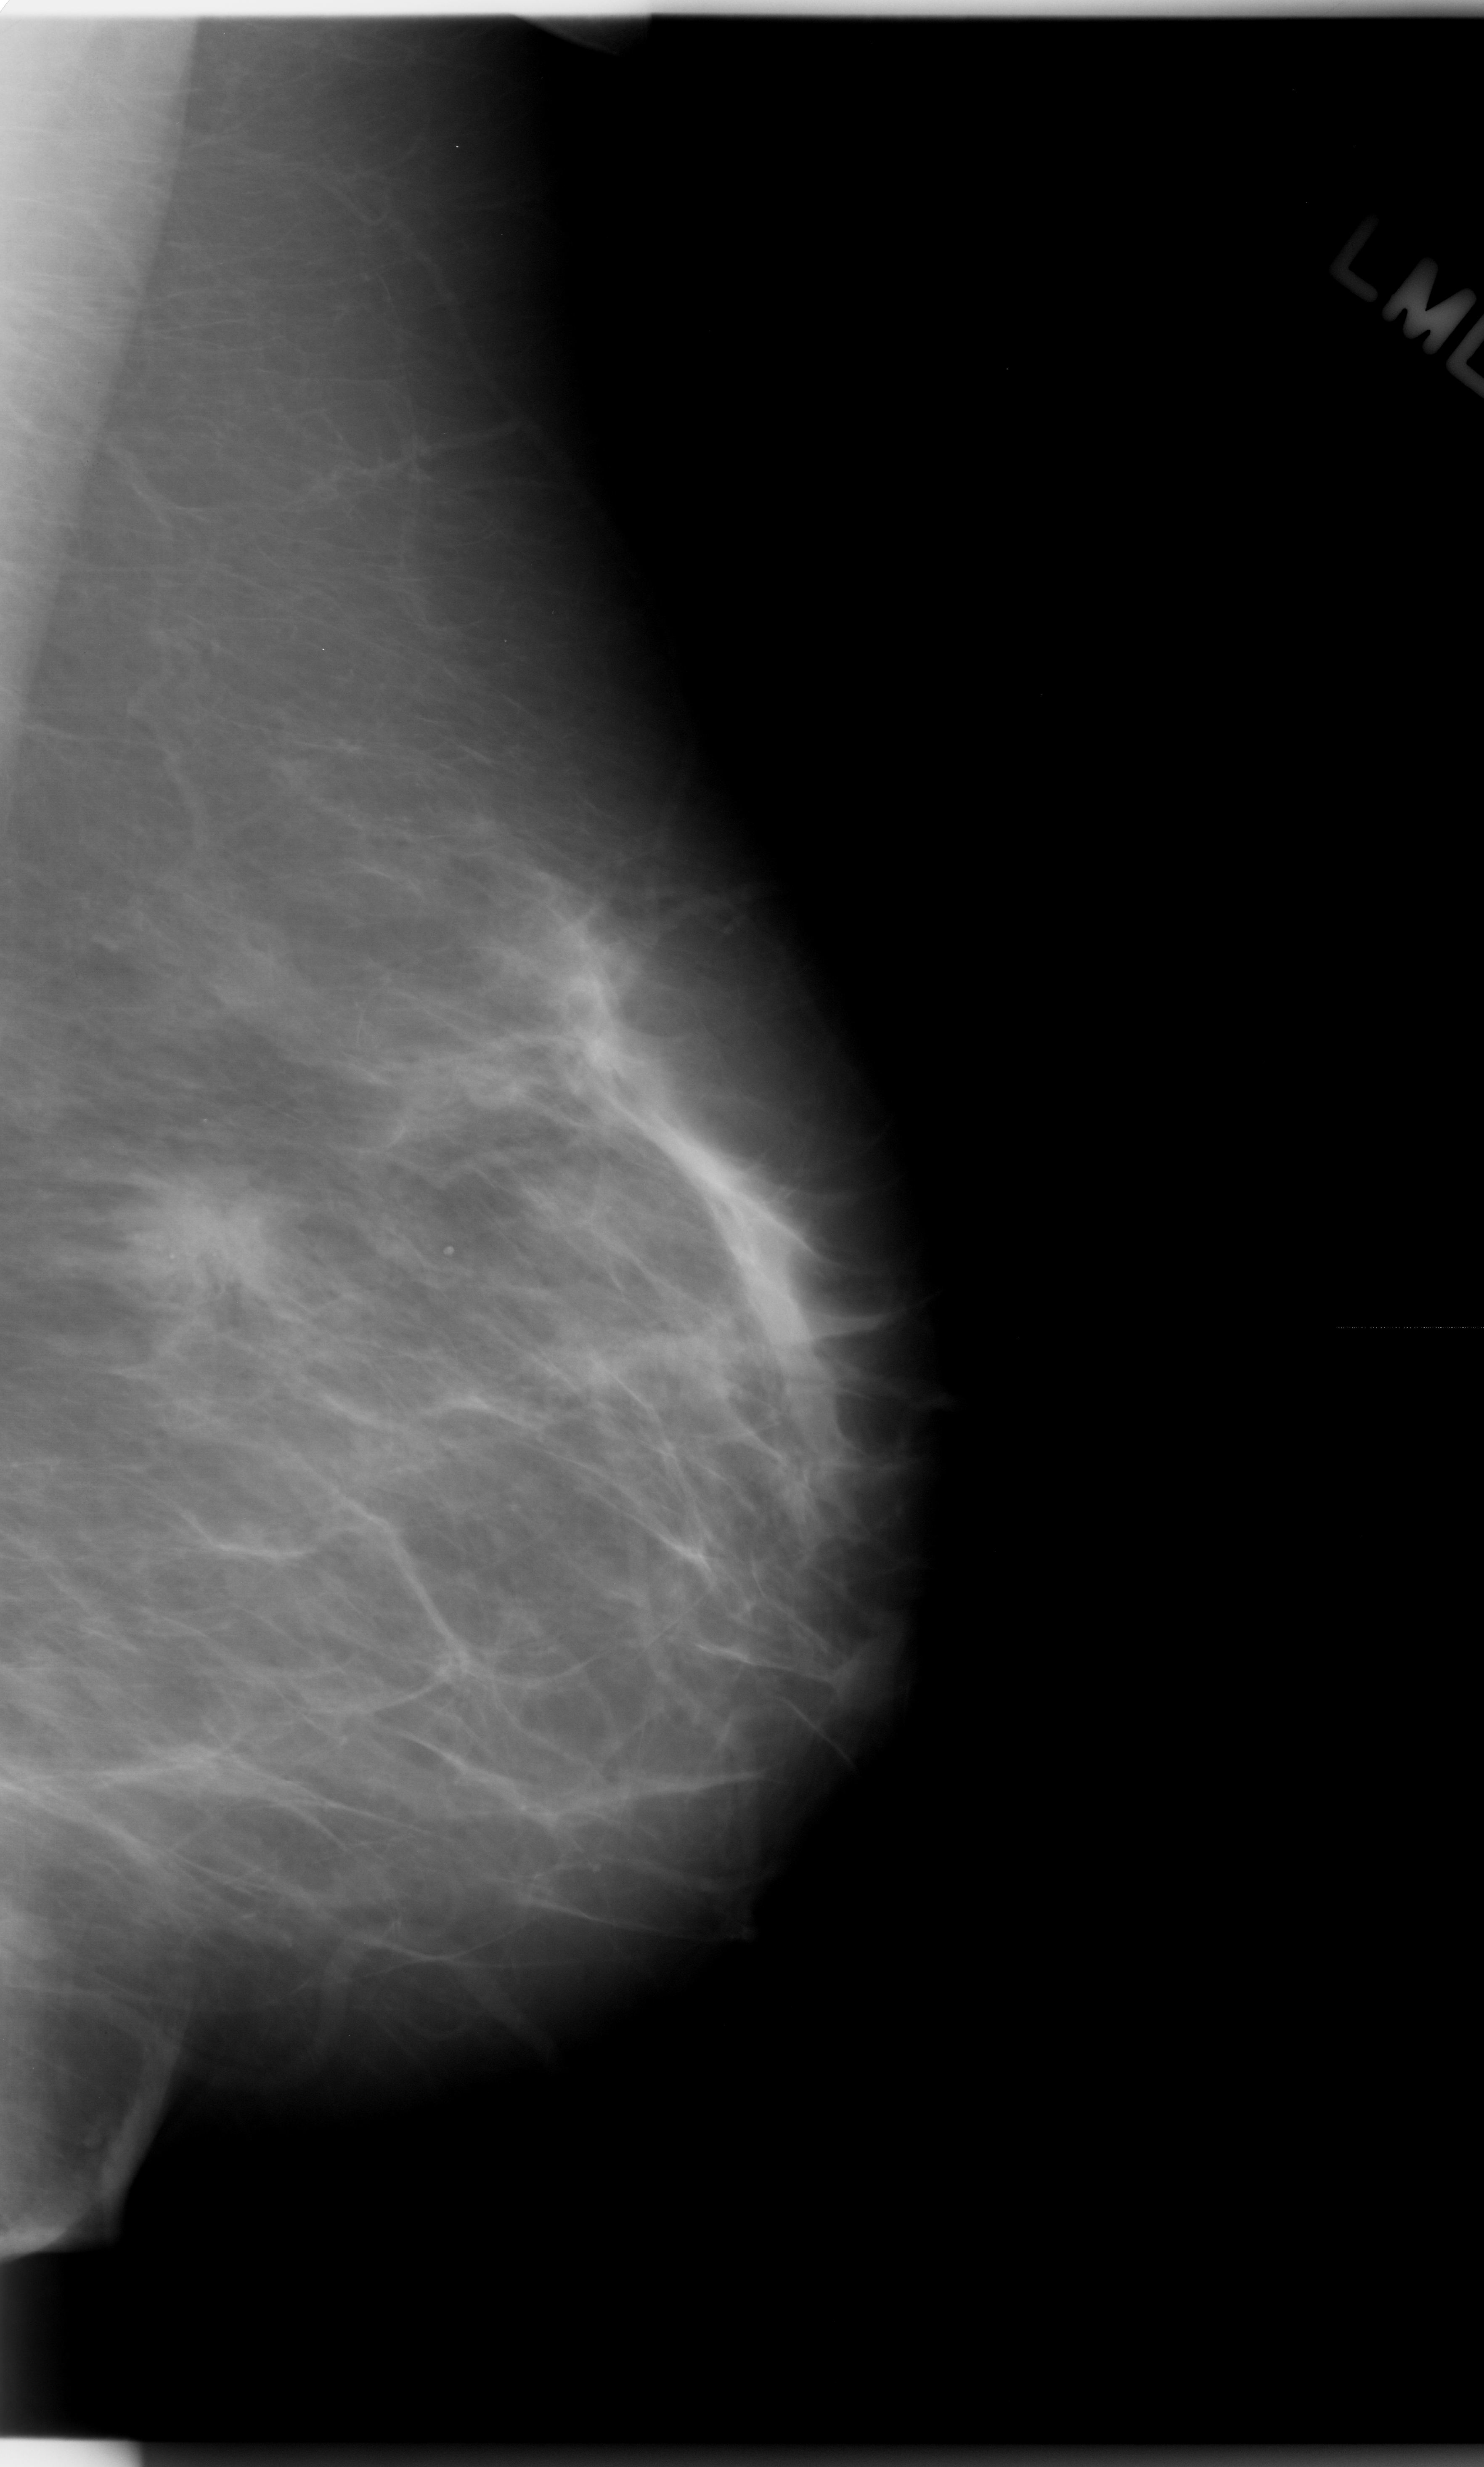
Mammogram (digitized film); left breast; mediolateral oblique (MLO) view; BI-RADS breast density category 1 (scale 1–4).
Abnormality record for this image: mass, shape irregular, margins spiculated; BI-RADS assessment category 5; pathology (as recorded): malignant.